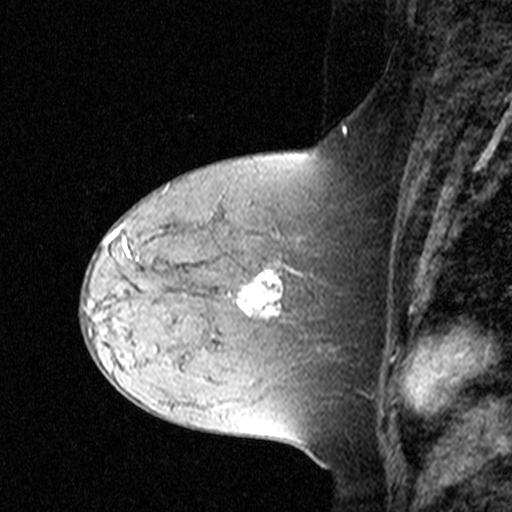
Breast MRI (dynamic contrast-enhanced), one sagittal slice. Position 16 of 44 along the scan axis. Dynamic contrast-enhanced study with each time point stored as its own series, time point 2 of 3 at this slice position (early post-contrast, ordered by acquisition time). 1.5 T. TE 4.5 ms, TR 11 ms. 3 mm slice thickness. 512 × 512 image matrix. Patient: female, 44 years. From the clinical record (not read from this slice): setting: breast cancer imaged before/during neoadjuvant chemotherapy; receptor status: triple-negative.
Annotated regions visible in this slice (semi-automatically segmented with operator editing):
- analysis volume of interest (the breast-tissue region the enhancement analysis was run in; not a lesion): box from (x=132, y=212) to (x=309, y=331) px
- tumour enhancement mask (voxels above the 90 % enhancement threshold inside the analysis volume of interest): (x=237, y=270)–(x=283, y=316)